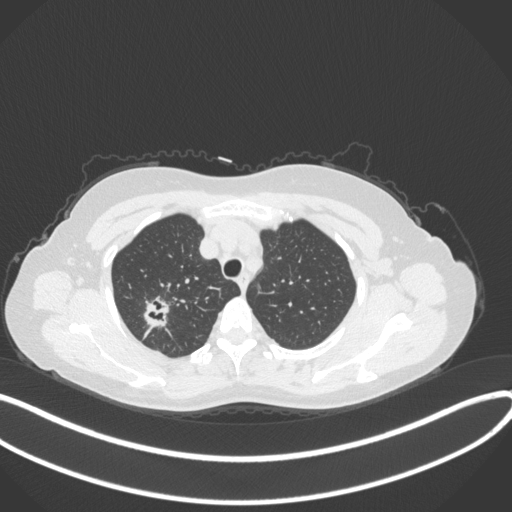
Chest CT, one axial slice. Slice 295 of 342 in the series (ordered by position). Reconstruction kernel B31f. Lung window (W 1500 / L -600 HU). 1 mm slice thickness. 512 × 512 image matrix, field of view 400 × 400 mm. Patient: female, 50 years. Case-level facts recorded for this patient, not image findings: clinical TNM (as recorded): T1c N0 M0.
Annotated regions visible in this slice (rectangle marked by the reading radiologist):
- lung tumour (recorded histology: adenocarcinoma): box from (x=139, y=289) to (x=171, y=332) px